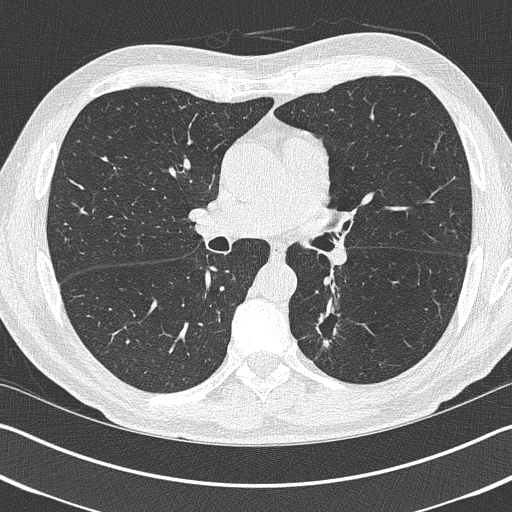
Low-dose screening chest CT, one axial slice; position 236 of 402 along the scan axis; 120 kVp; lung window (W 1500 / L -600 HU); 1 mm slice thickness; 512 × 512 image matrix.
Outlined on this slice (expert manual segmentation):
- lesion 1 (tumor, lower lobe of left lung): bounding box [x1, y1, x2, y2] px = [316, 309, 336, 347]